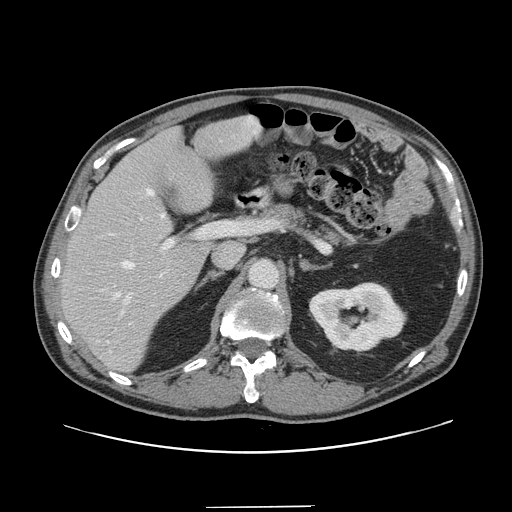
Contrast-enhanced abdominal CT, one axial slice. Slice 87 of 139 in the series (ordered by position). 120 kVp. Intravenous contrast given. Soft-tissue window (W 400 / L 40 HU). 512 × 512 image matrix, field of view 397 × 397 mm. Male patient, age 64 years. From the clinical record (not read from this slice): diagnosis: colorectal cancer liver metastases, imaged before liver resection; multiple liver metastases: yes; largest metastasis: 3.5 cm; disease in both lobes: yes.
Outlined on this slice (manually delineated by an expert):
- hepatic veins: bounding box (x1, y1, x2, y2) in pixels: (114, 140, 221, 324)
- liver: (61, 116, 260, 371)
- planned liver remnant (the part of the liver to remain after resection): (62, 117, 259, 371)
- portal vein (with intrahepatic branches): (110, 222, 218, 315)